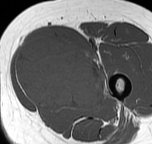
MRI of an extremity soft-tissue mass, one axial slice; position 25 of 57 along the scan axis; MR volume resampled by the dataset authors to the PET/CT grid (not the native acquisition matrix); 3.27 mm slice thickness; 152 × 144 image matrix. Female patient. Case-level facts recorded for this patient, not image findings: histological type: pleiomorphic leiomyosarcoma; grade: intermediate; site of the primary tumour: left thigh.
Outlined on this slice (expert contour drawn on MRI and transferred to this co-registered scan by the dataset authors):
- gross tumour volume including surrounding oedema: bounding box (x1, y1, x2, y2) in pixels: (15, 39, 110, 111)
- gross tumour volume (mass): (15, 39, 105, 107)